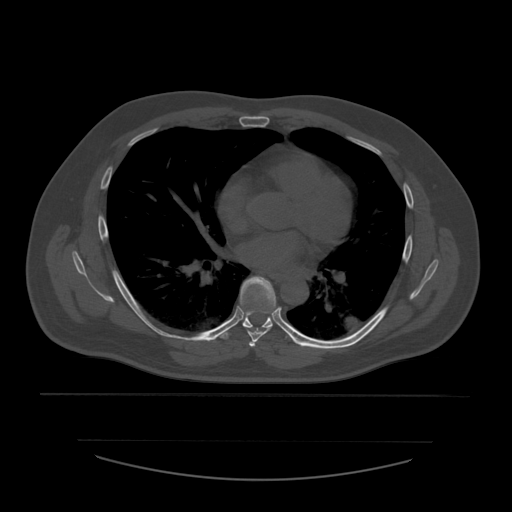
CT including the spine, one axial slice. Position 369 of 532 along the scan axis. Reconstruction kernel STANDARD. 120 kVp. Bone window (W 1800 / L 400 HU). 1.25 mm slice thickness. 512 × 512 image matrix. Patient age 44 years. Case-level facts recorded for this patient, not image findings: primary cancer: soft tissue sarcoma.
Annotated regions visible in this slice (semi-automatic segmentation, software-assisted and operator-edited):
- T5 vertebra: bounding box <249,341,255,347> (left, top, right, bottom; pixels)
- T6 vertebra: <240,277,276,346>
- T7 vertebra: <217,288,292,339>